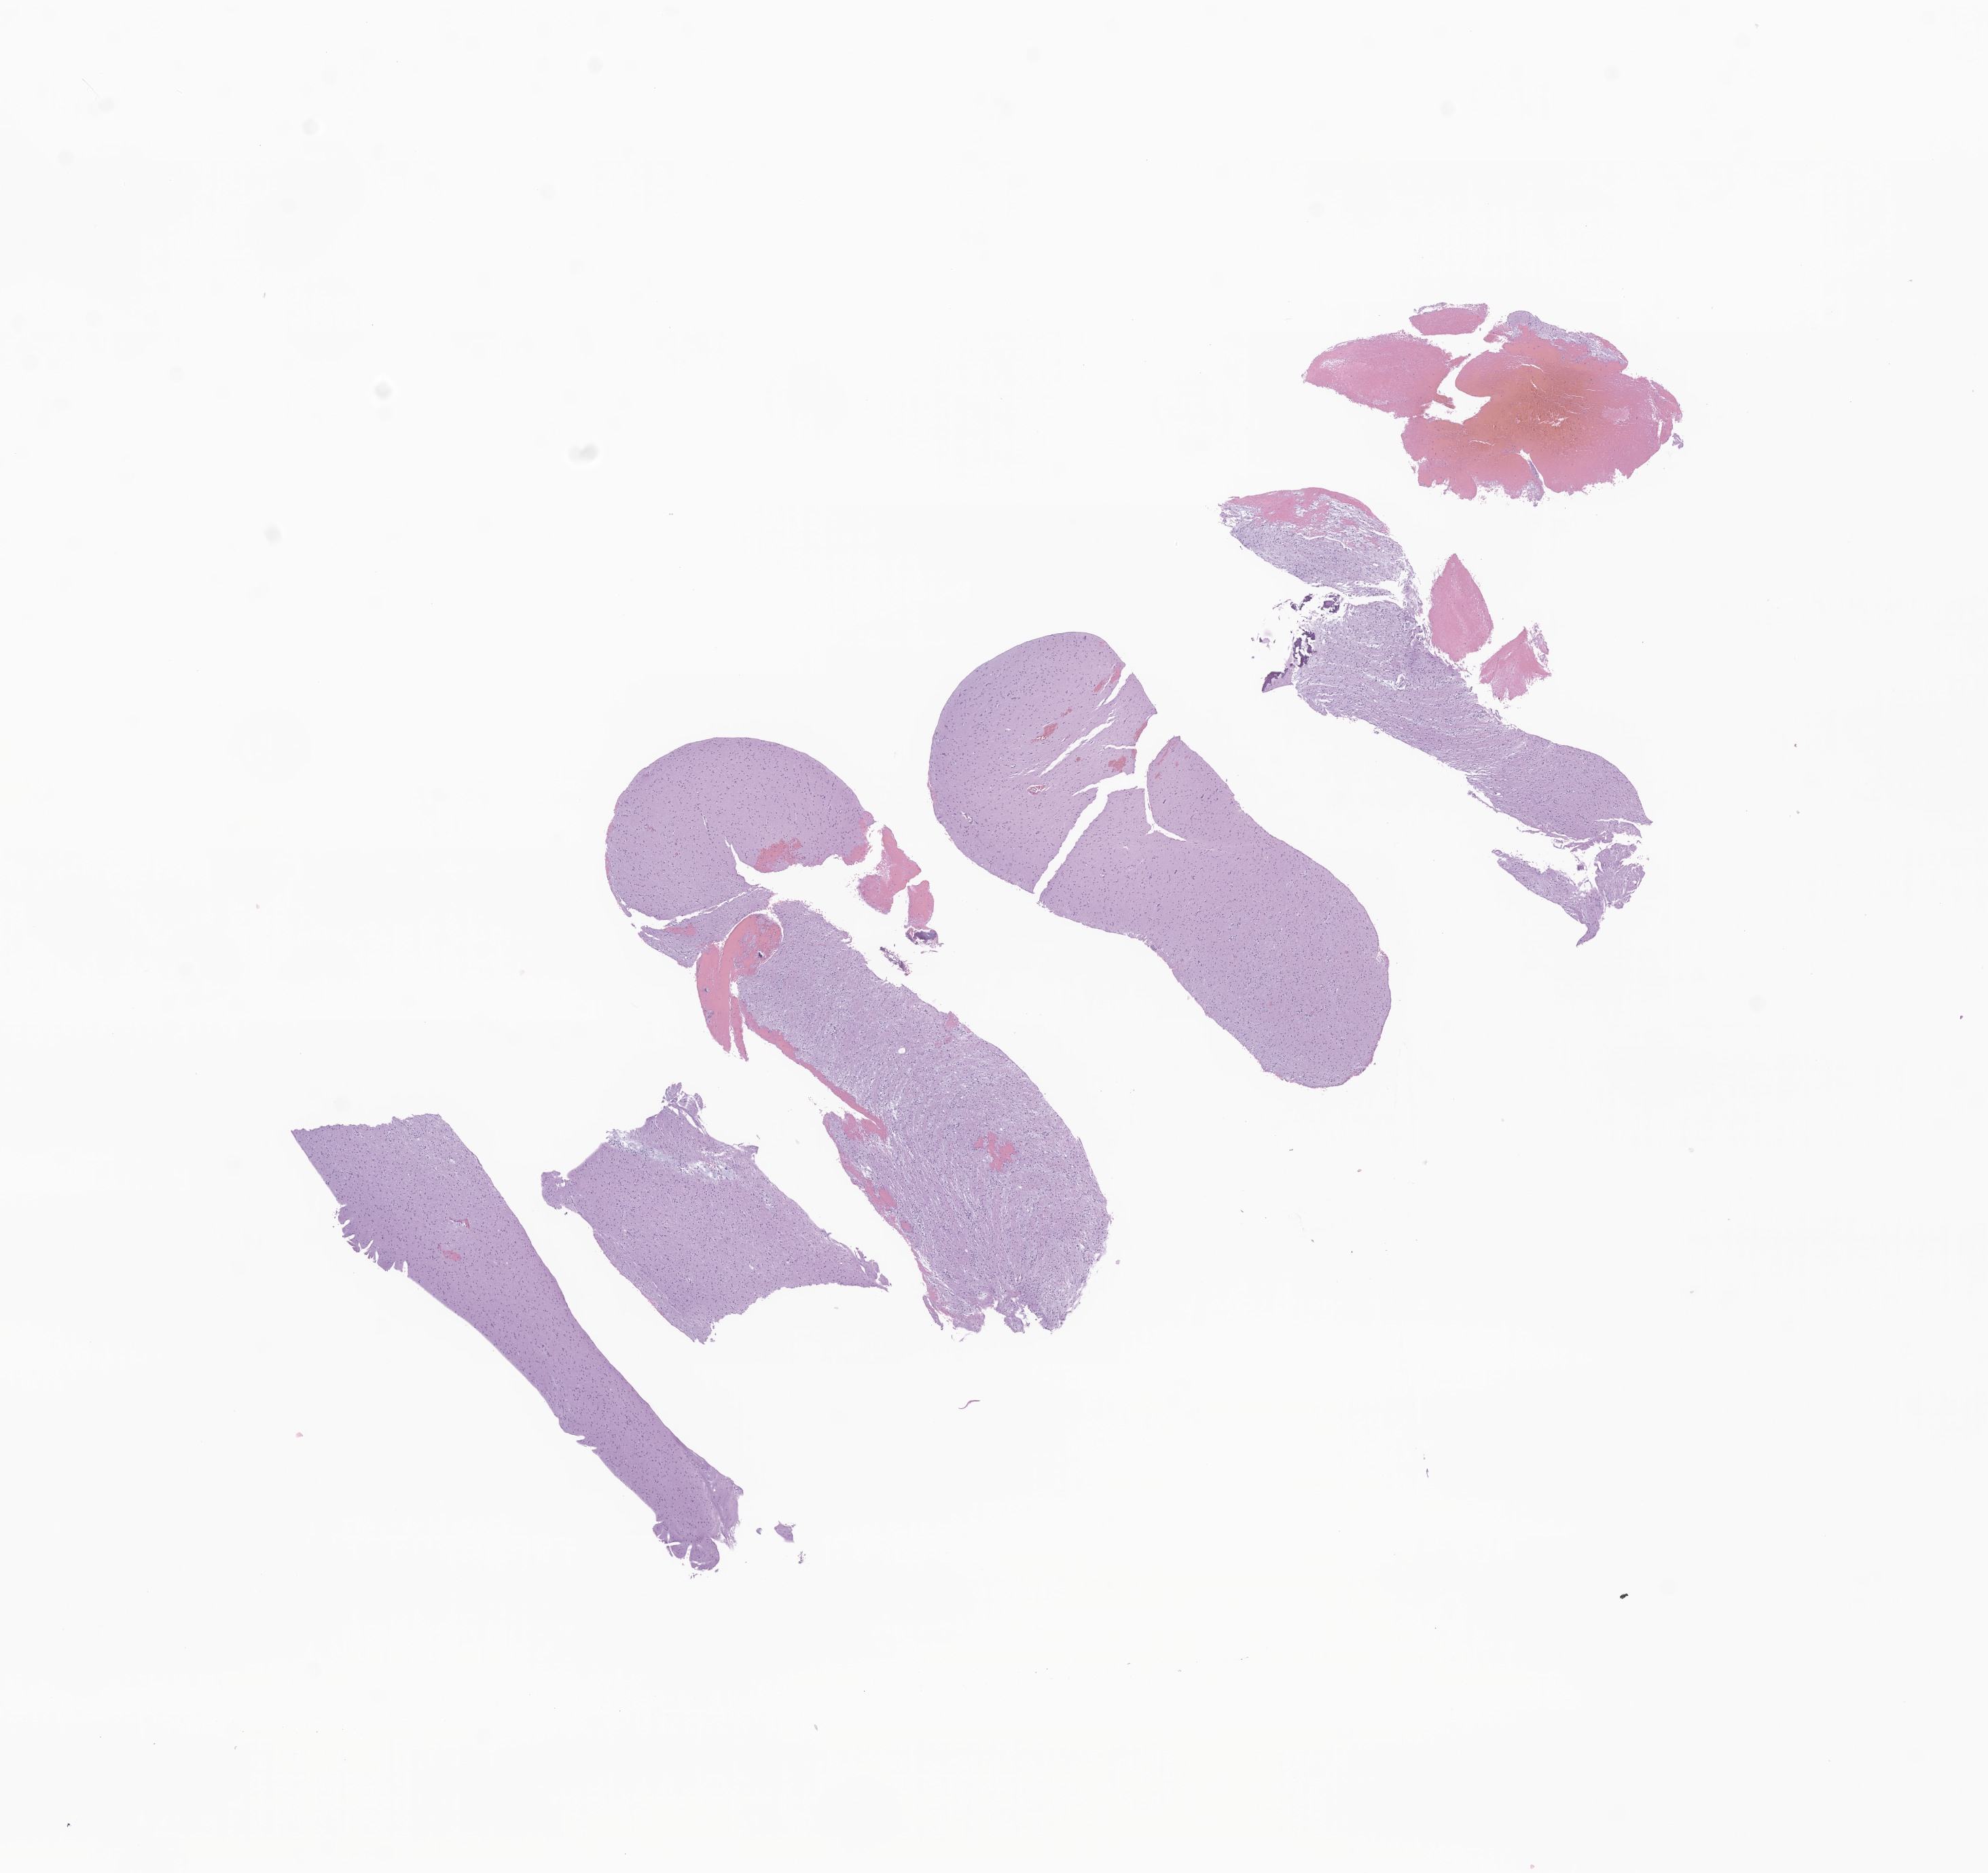
Digitized haematoxylin and eosin-stained section of tumor tissue from the brain, a low-resolution overview of the entire scanned area, about 12.3 x 11.6 mm, formalin-fixed, paraffin-embedded (FFPE) tissue. Male patient, age 130 months (10 years 10 months).
Diagnosis: Neuroepithelioma, NOS.